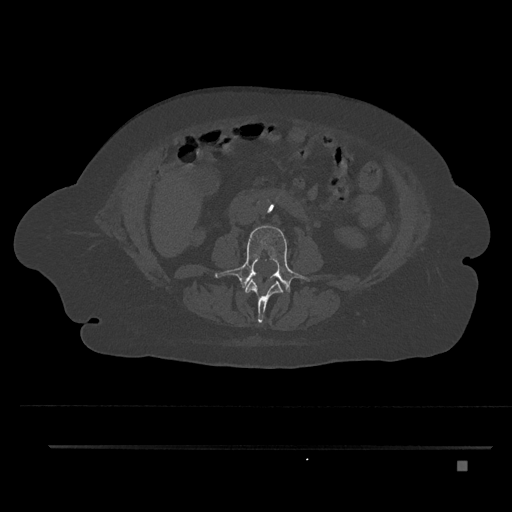
CT including the spine, one axial slice. Slice 140 of 797 in the series (ordered by position). Reconstruction kernel Br40s/3. Bone window (W 1800 / L 400 HU). 0.5 mm slice thickness. 512 × 512 image matrix, field of view 437 × 437 mm. Female patient, age 76 years. Case-level facts recorded for this patient, not image findings: primary cancer: lung; vertebrae with lytic lesions (as recorded): T11, L3.
Annotated regions visible in this slice (semi-automatic segmentation, software-assisted and operator-edited):
- L2 vertebra: bounding box <245,278,283,323> (left, top, right, bottom; pixels)
- L3 vertebra: <215,225,309,293>